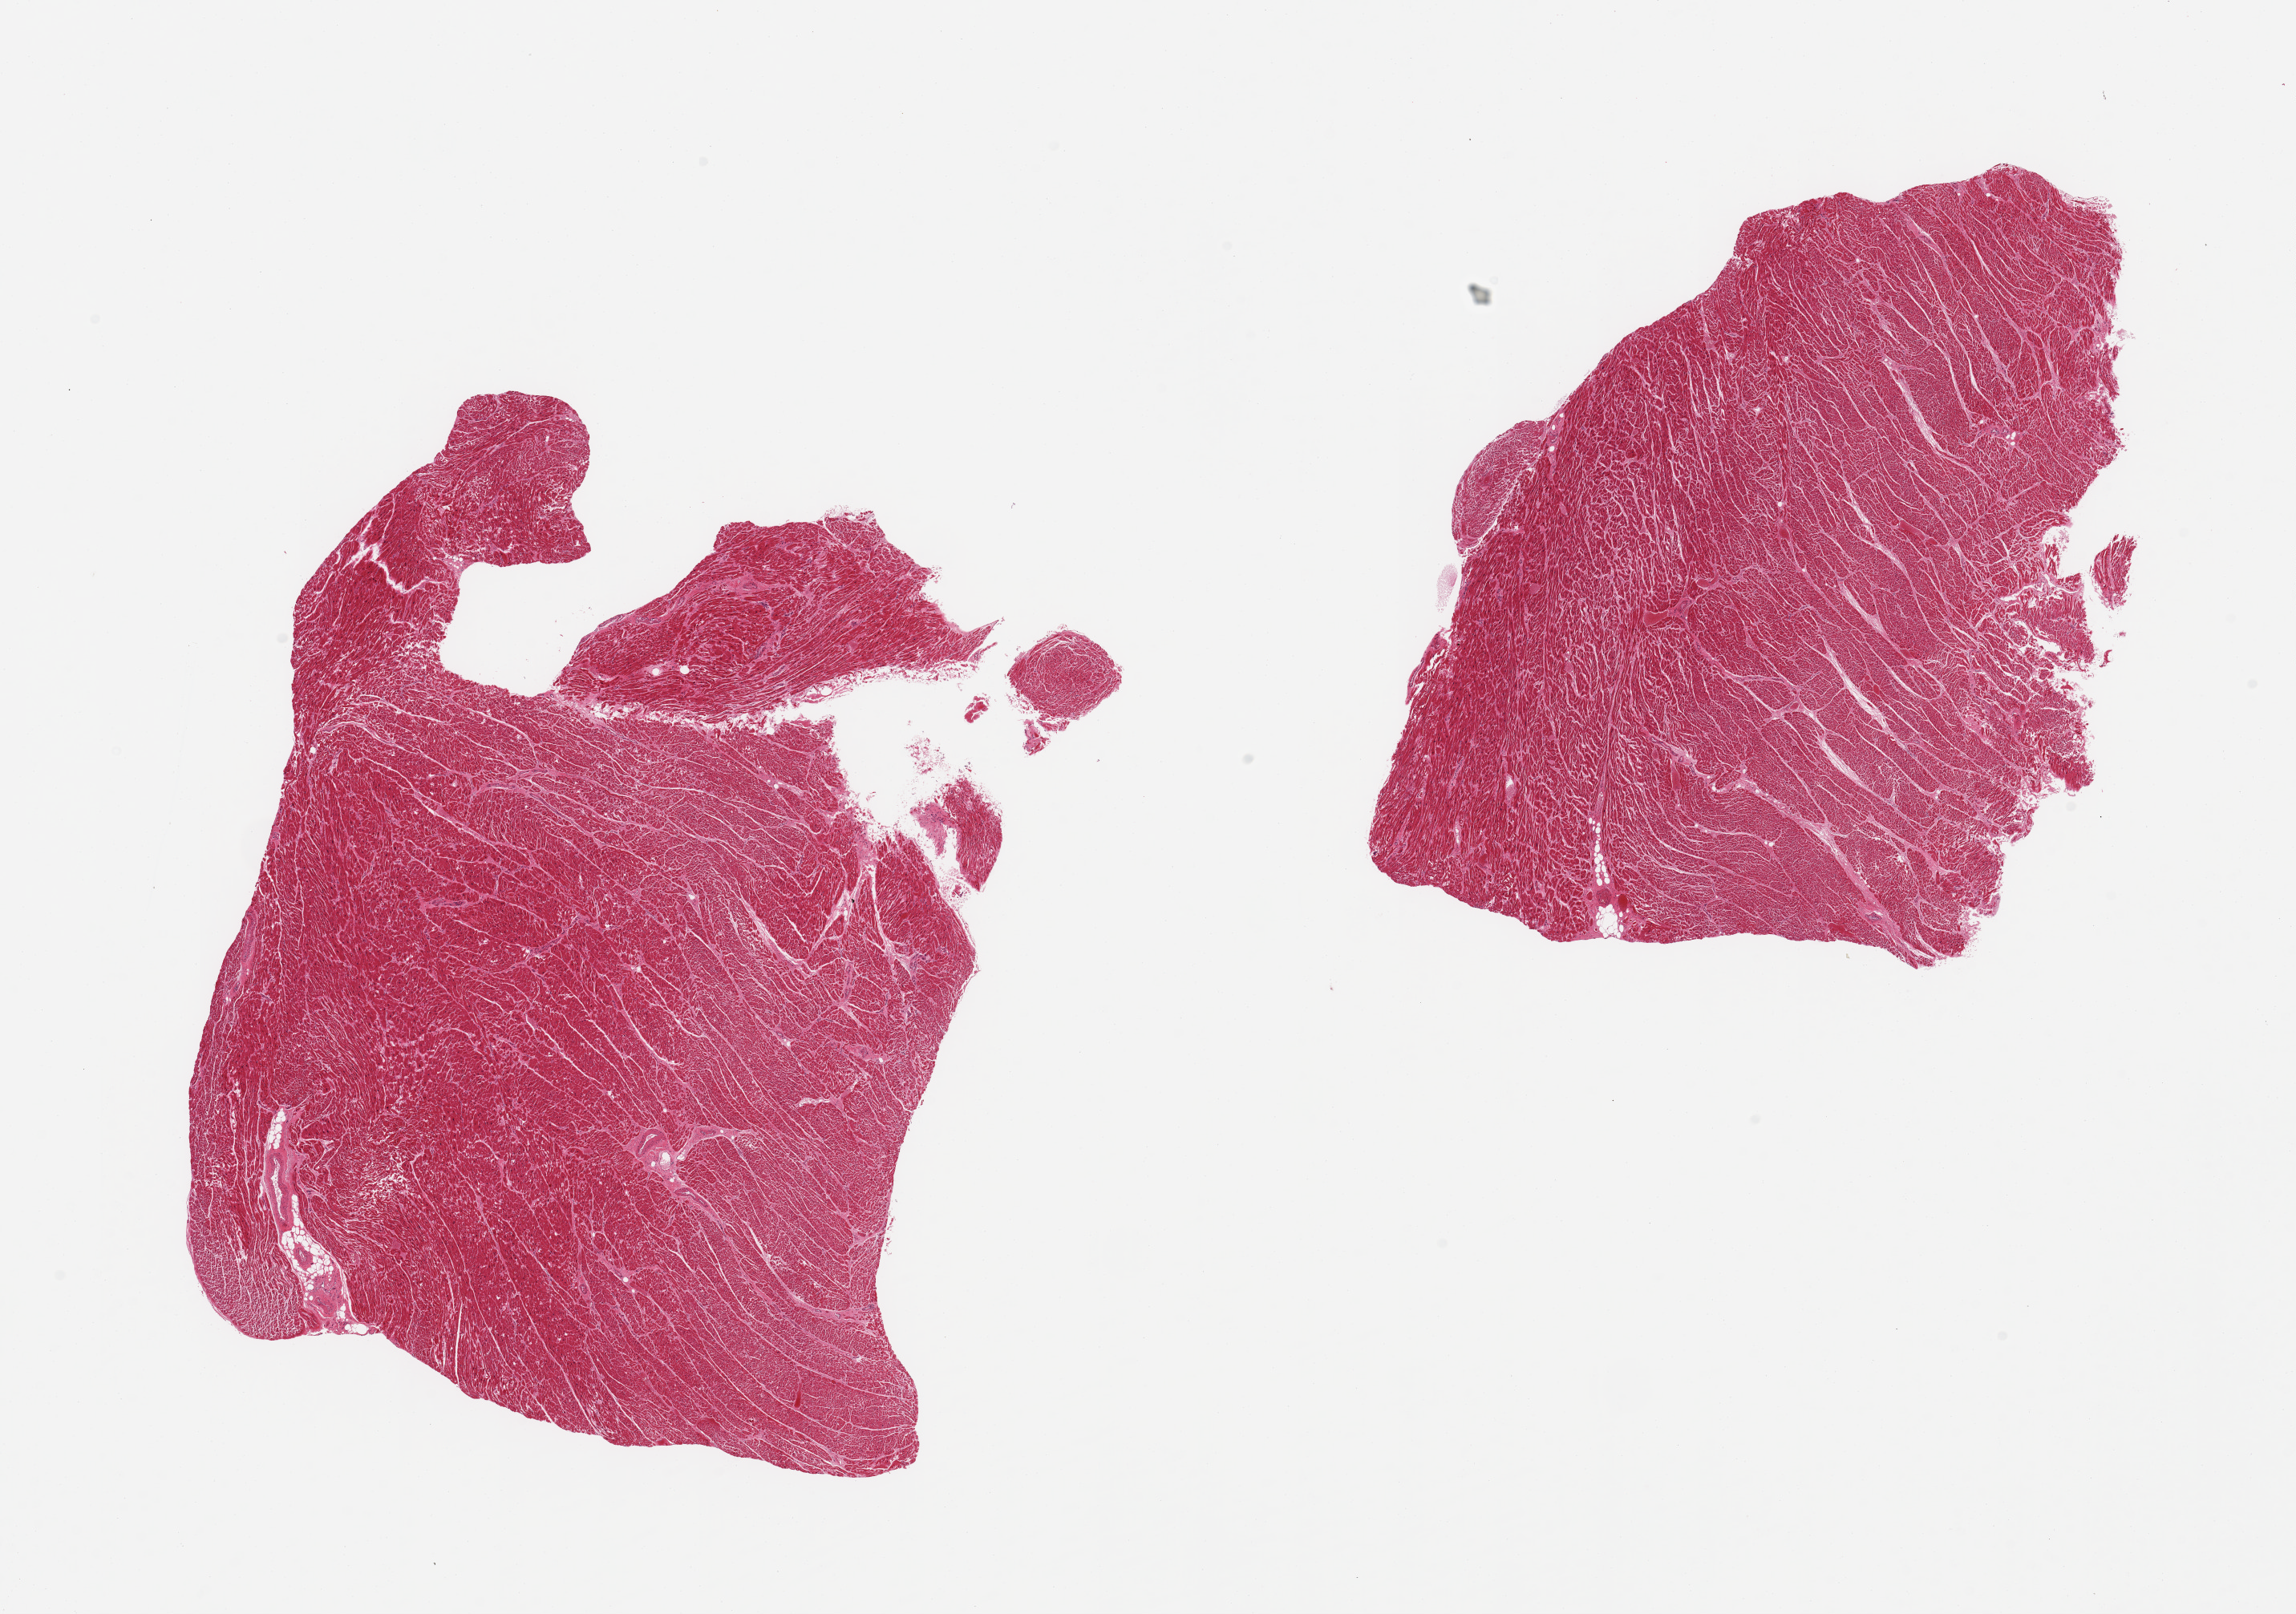
Whole-slide image, H&E stain, brightfield — whole scanned area (about 22.6 x 15.9 mm, slide scanned at 20x) shown as a low-resolution overview; PAXgene-fixed paraffin-embedded (PFPE) section; sampled site (target tissue): heart; donor tissue sample. Donor: male.
Reviewer comment on this tissue sample: 2 pieces; mild interstitial fibrosis.